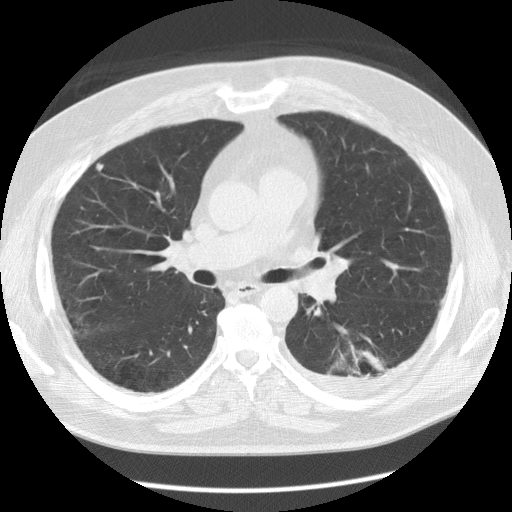
Low-dose screening chest CT, axial slice. Baseline screening round. Lung window (W 1500 / L -600 HU). 2.5 mm slice thickness. Standard (soft-tissue) reconstruction kernel (STANDARD). Slice 53 of 126 in the series. Male participant, aged 56 years at enrolment. Former smoker at enrolment.
Lesion marked by an expert reader, bounding box [x1, y1, x2, y2] px = [322, 337, 394, 391]. The screening reader recorded 4 non-calcified nodules or masses ≥4 mm on this exam (left lower lobe, left lower lobe, right middle lobe, left upper lobe); which of them this box marks is not recorded. Official screen result: positive, change unspecified: nodule(s) >= 4 mm or enlarging nodule(s), mass(es), or other non-specific abnormalities suspicious for lung cancer. Participant outcome: lung cancer diagnosed 173 days after this screen — non-small cell carcinoma, left lower lobe, stage IV (AJCC 6th edition), 50 mm at pathology.